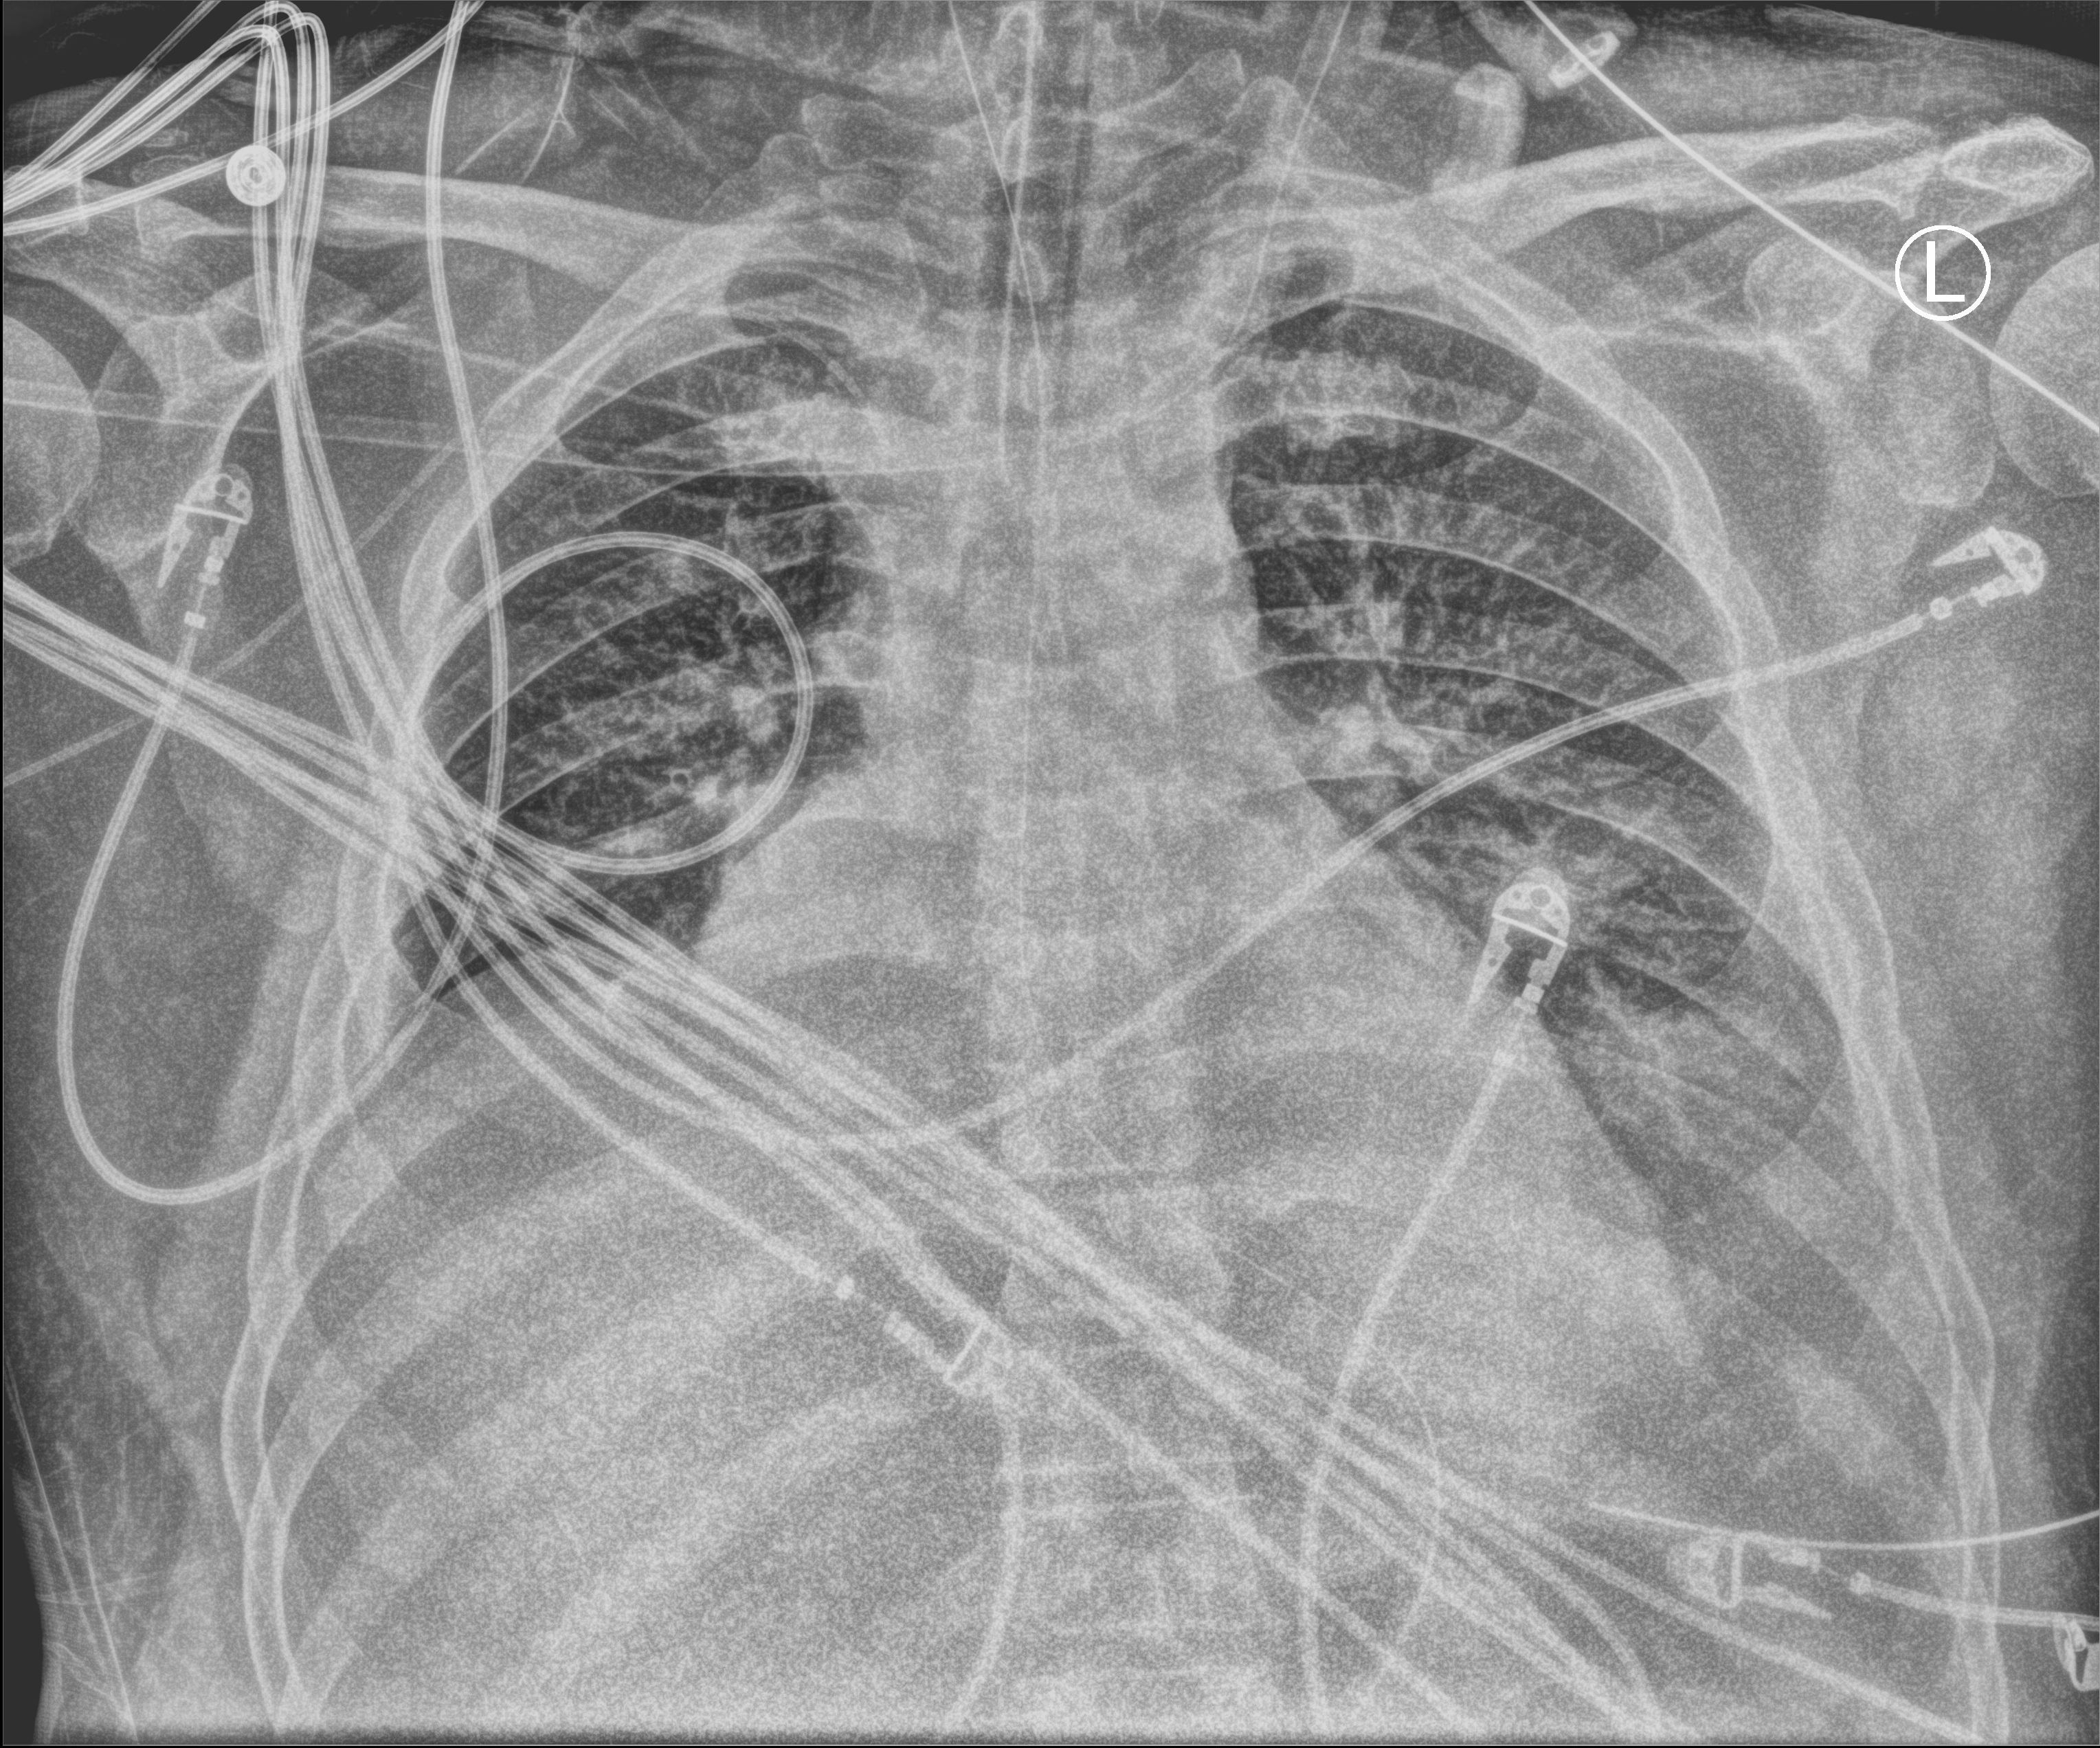
Bedside chest radiograph (computed radiography); anteroposterior (AP) projection. Patient hospitalised with COVID-19; male, aged 18–59 years.
Hospital-stay facts (about this admission, not read from this image; timing relative to this image not recorded): mechanically ventilated during this hospital stay: yes; admitted to intensive care during this hospital stay: yes.